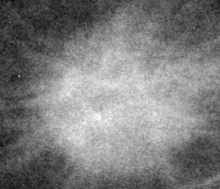
Cropped region of a digitized screen-film mammogram centred on a radiologist-marked abnormality; right breast; MLO view.
- Mass, shape irregular, margins spiculated; BI-RADS assessment category 4; subtlety rating 5 on a 1 (subtle) to 5 (obvious) scale; pathology result (as recorded, not read from the image): malignant.